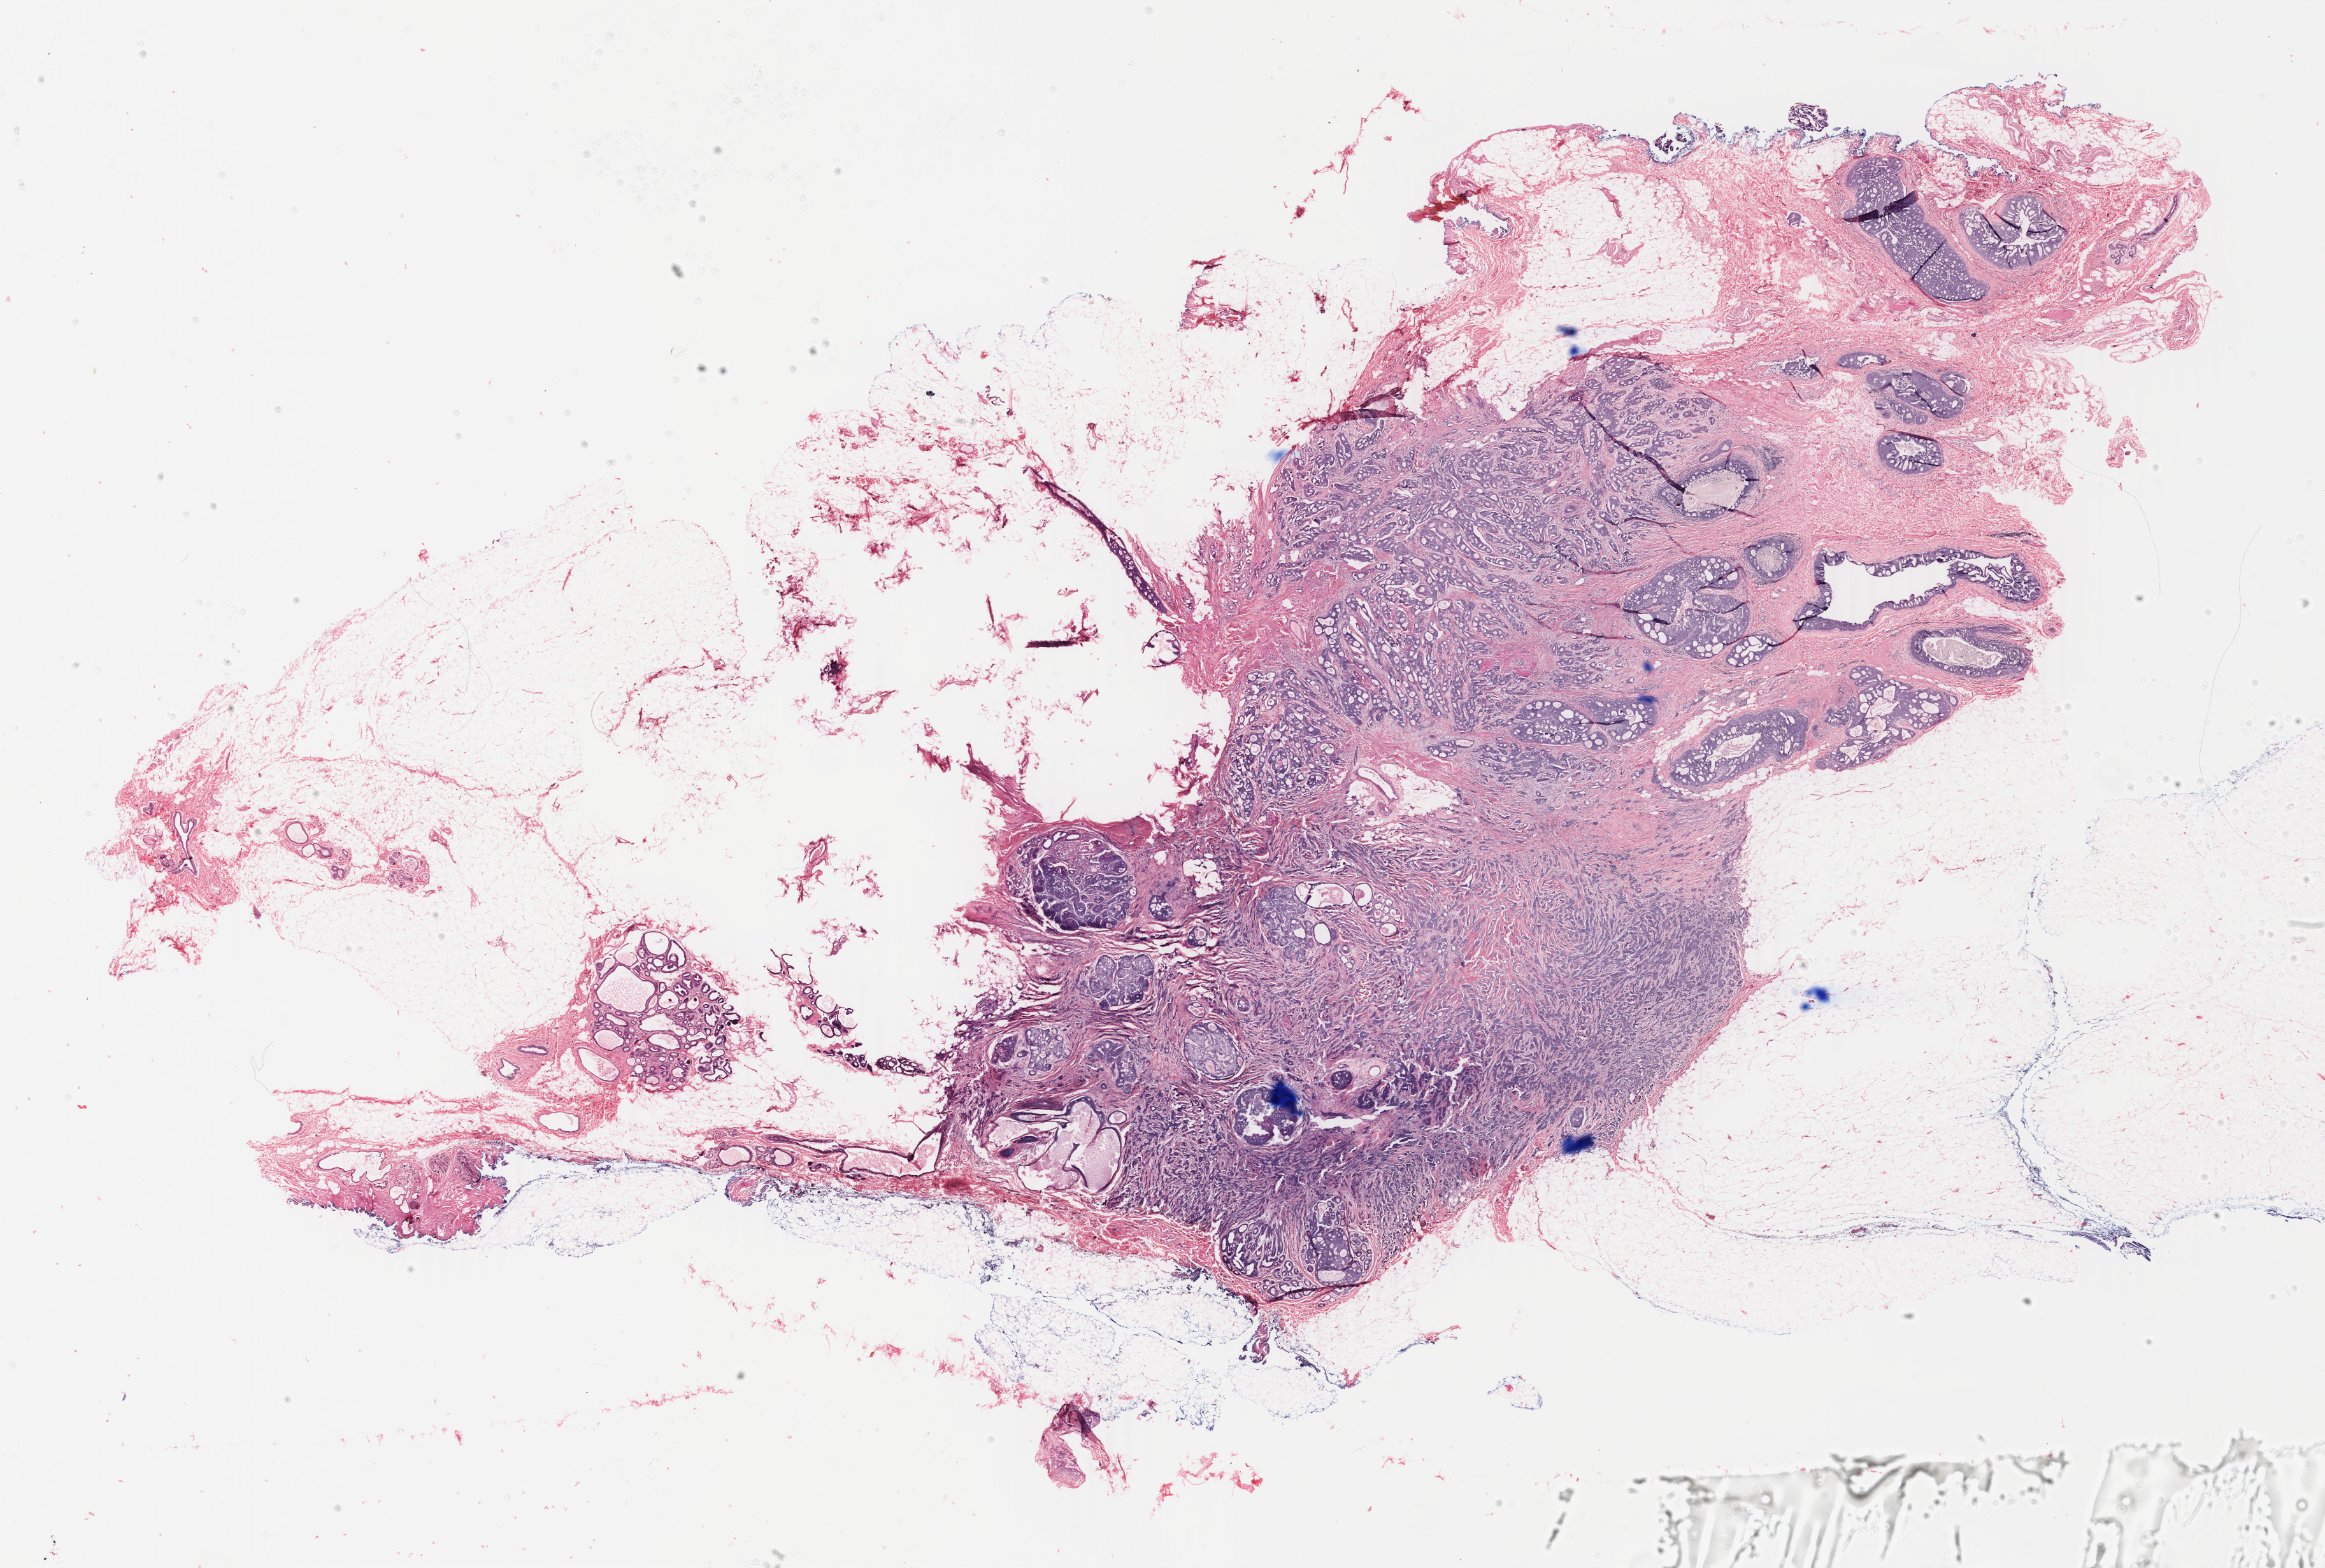
Digitized H&E-stained tissue section (whole slide), low-resolution overview of the scanned area, about 29.0 x 19.6 mm, FFPE section, primary tumour sample from the breast. Female patient; age at initial diagnosis 49 years.
- histologic diagnosis: Infiltrating duct carcinoma, NOS
- AJCC pathologic stage: IIB (3rd edition)
- laterality: right
- lymph nodes positive (case pathology): 5 of 13 examined